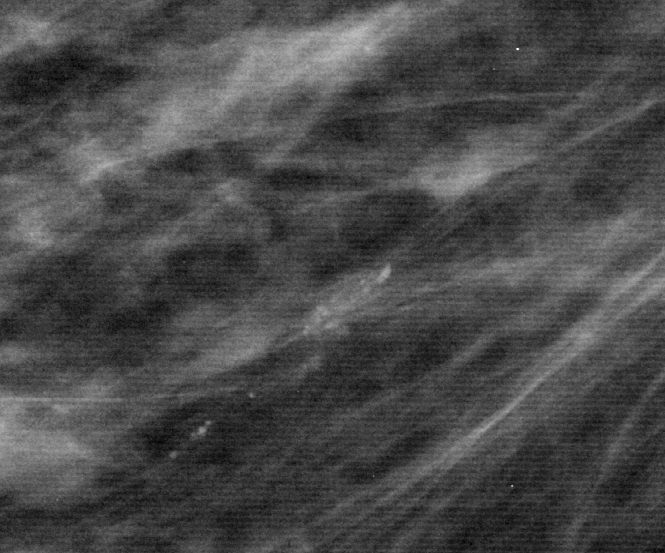
Crop from a digitized film mammogram around one marked abnormality; right breast; MLO view.
Calcifications, morphology fine linear branching, distribution linear; BI-RADS assessment category 4; pathology (as recorded): benign.